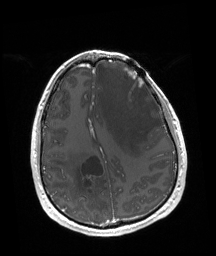
Brain MRI from a brain-tumour surgery series, one axial slice. Position 60 of 192 along the scan axis. T1-weighted post-contrast. 1 mm slice thickness. 216 × 256 image matrix. From the clinical record (not read from this slice): tumour location: Left Frontal.
Outlined on this slice (expert manual segmentation):
- tumour: bounding box <124,66,144,87> (left, top, right, bottom; pixels)